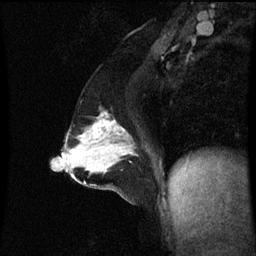
Breast MRI (dynamic contrast-enhanced), one sagittal slice; slice 33 of 60 in the series (ordered by position); dynamic contrast-enhanced series, image 2 of 3 at this slice position (ordered by acquisition); 1.5 T; TE 4.2 ms, TR 8.9 ms; 256 × 256 image matrix. Patient: female, 47 years. From the clinical record (not read from this slice): setting: breast cancer imaged before/during neoadjuvant chemotherapy; receptor status: HR-positive, HER2-negative.
Outlined on this slice (semi-automatically segmented with operator editing):
- analysis volume of interest (the breast-tissue region the enhancement analysis was run in; not a lesion): box from (x=71, y=114) to (x=138, y=163) px
- tumour enhancement mask (voxels above the 70 % enhancement threshold inside the analysis volume of interest): (x=93, y=120)–(x=133, y=155)